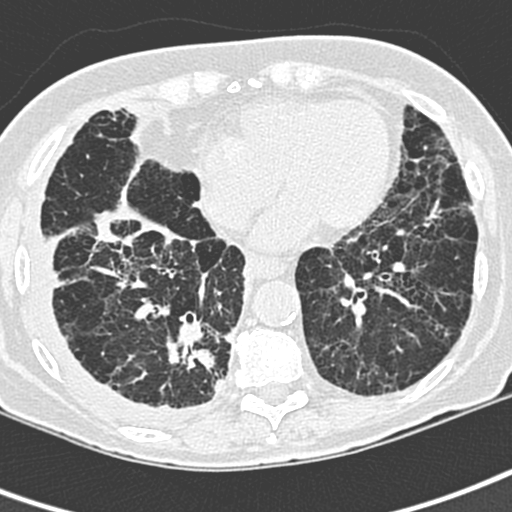
Low-dose screening chest CT, one axial slice. Position 90 of 220 along the scan axis. 120 kVp. Lung window (W 1500 / L -600 HU). 512 × 512 image matrix, field of view 288 × 288 mm.
Structures marked on this image (manually delineated by an expert):
- lesion 1 (tumor, lower lobe of right lung): bounding box <168,344,215,371> (left, top, right, bottom; pixels)